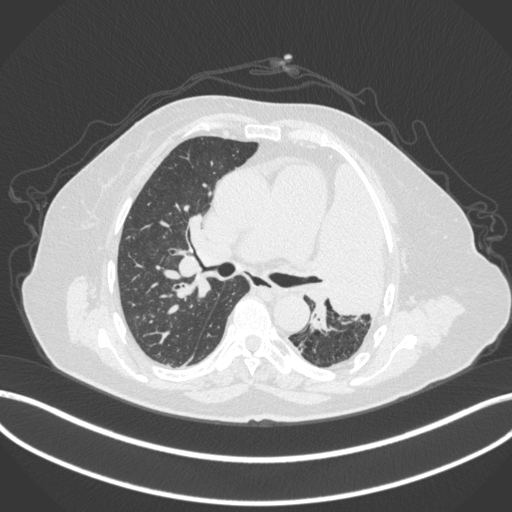
Chest CT, one axial slice. Position 234 of 399 along the scan axis. Reconstruction kernel B31f. Lung window (W 1500 / L -600 HU). 512 × 512 image matrix, field of view 400 × 400 mm. Female patient, age 75 years. From the clinical record (not read from this slice): clinical TNM (as recorded): T3 N3 M1.
Structures marked on this image (rectangle marked by the reading radiologist):
- lung tumour (recorded histology: adenocarcinoma): box from (x=316, y=157) to (x=390, y=325) px